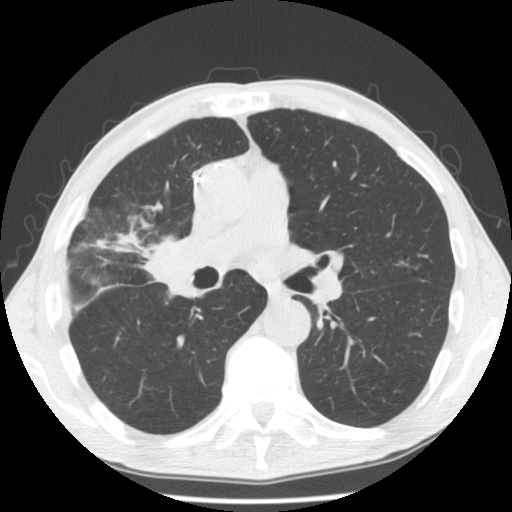
Low-dose screening chest CT, one axial slice; slice 74 of 132 in the series (ordered by position); reconstruction kernel STANDARD; lung window (W 1500 / L -600 HU); 512 × 512 image matrix, field of view 334 × 334 mm.
Annotated regions visible in this slice (outlined manually by an expert reader):
- lesion 1 (tumor, hilum of right lung): bounding box (x1, y1, x2, y2) in pixels: (145, 241, 183, 281)